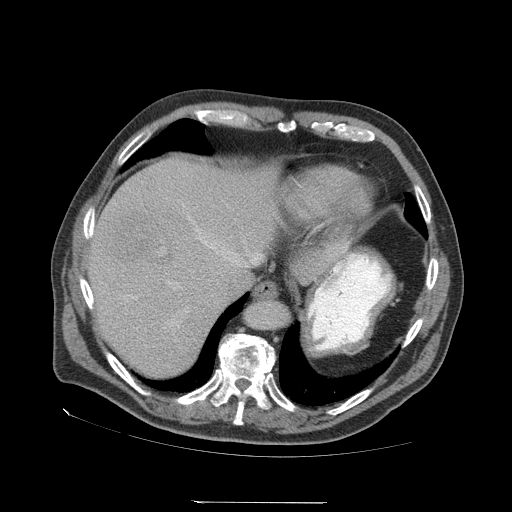
Contrast-enhanced abdominal CT (liver protocol), one axial slice. Reconstruction kernel STANDARD. 140 kVp. Soft-tissue window (W 400 / L 40 HU). 2.5 mm slice thickness. 512 × 512 image matrix. Case-level facts recorded for this patient, not image findings: diagnosis: hepatocellular carcinoma (patient treated with transarterial chemoembolisation; whether this scan precedes or follows treatment is not stated here); TNM stage (as recorded): Stage-I; Child-Pugh class: A; tumour differentiation: well differentiated.
Outlined on this slice (semi-automatic segmentation, software-assisted and operator-edited):
- abdominal aorta: bounding box [x1, y1, x2, y2] px = [247, 301, 288, 328]
- liver parenchyma outside the tumour (the mass and vessels are separate outlines, so this box may not span the whole liver): [88, 158, 280, 376]
- mass: [92, 208, 170, 266]
- liver vessels: [91, 204, 261, 325]